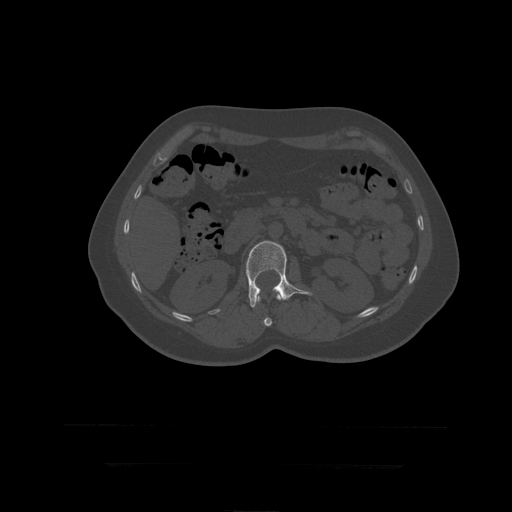
CT including the spine, one axial slice. Position 155 of 399 along the scan axis. Reconstruction kernel STANDARD. Bone window (W 1800 / L 400 HU). 512 × 512 image matrix, field of view 450 × 450 mm. Patient age 41 years. From the clinical record (not read from this slice): primary cancer: breast.
Annotated regions visible in this slice (semi-automatic segmentation, software-assisted and operator-edited):
- L1 vertebra: bounding box (x1, y1, x2, y2) in pixels: (256, 294, 281, 327)
- L2 vertebra: (246, 241, 312, 308)